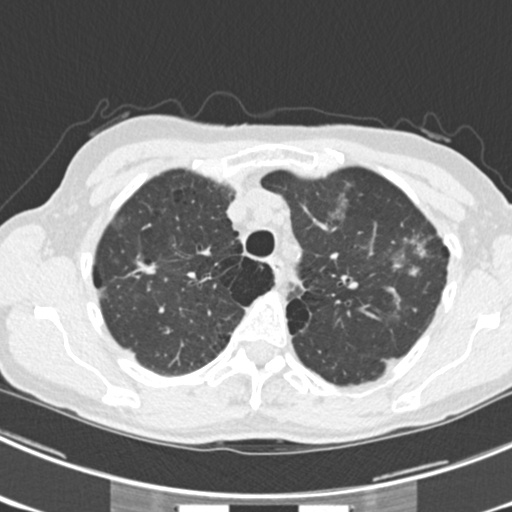
Axial slice from a low-dose chest CT screening exam, third annual screen, lung window (W 1500 / L -600 HU), 2 mm slice thickness, standard (soft-tissue) reconstruction kernel (B30f), slice 52 of 225 in the series, 512 × 512 image matrix. Female participant, aged 63 years at enrolment. Current smoker at enrolment.
Lesion marked by an expert reader, bounding box [x1, y1, x2, y2] px = [378, 220, 452, 280]. The screening reader recorded 9 non-calcified nodules or masses ≥4 mm on this exam (left upper lobe, right upper lobe, left upper lobe, left lower lobe, right middle lobe, left lower lobe, left lower lobe, right lower lobe, right lower lobe); which of them this box marks is not recorded. Official screen result: positive, other. Later outcome: lung cancer diagnosed 15 days after this screen — bronchiolo-alveolar adenocarcinoma, NOS, right upper lobe, right middle lobe, right lower lobe, left upper lobe, left lower lobe, moderately differentiated (G2), stage IV (AJCC 6th edition).